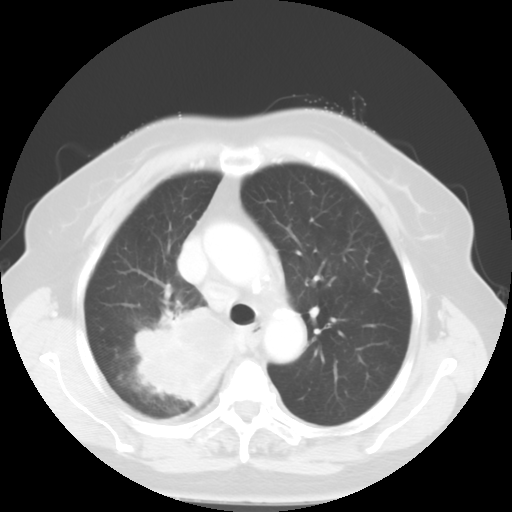
Chest CT, one axial slice. Position 38 of 52 along the scan axis. Reconstruction kernel STANDARD. 120 kVp. Lung window (W 1500 / L -600 HU). 5 mm slice thickness. 512 × 512 image matrix, field of view 333 × 333 mm. Patient: female, 81 years. From the clinical record (not read from this slice): clinical TNM (as recorded): T4 N3 M1b.
Outlined on this slice (rectangle marked by the reading radiologist):
- lung tumour (recorded histology: adenocarcinoma): bounding box <134,300,239,409> (left, top, right, bottom; pixels)